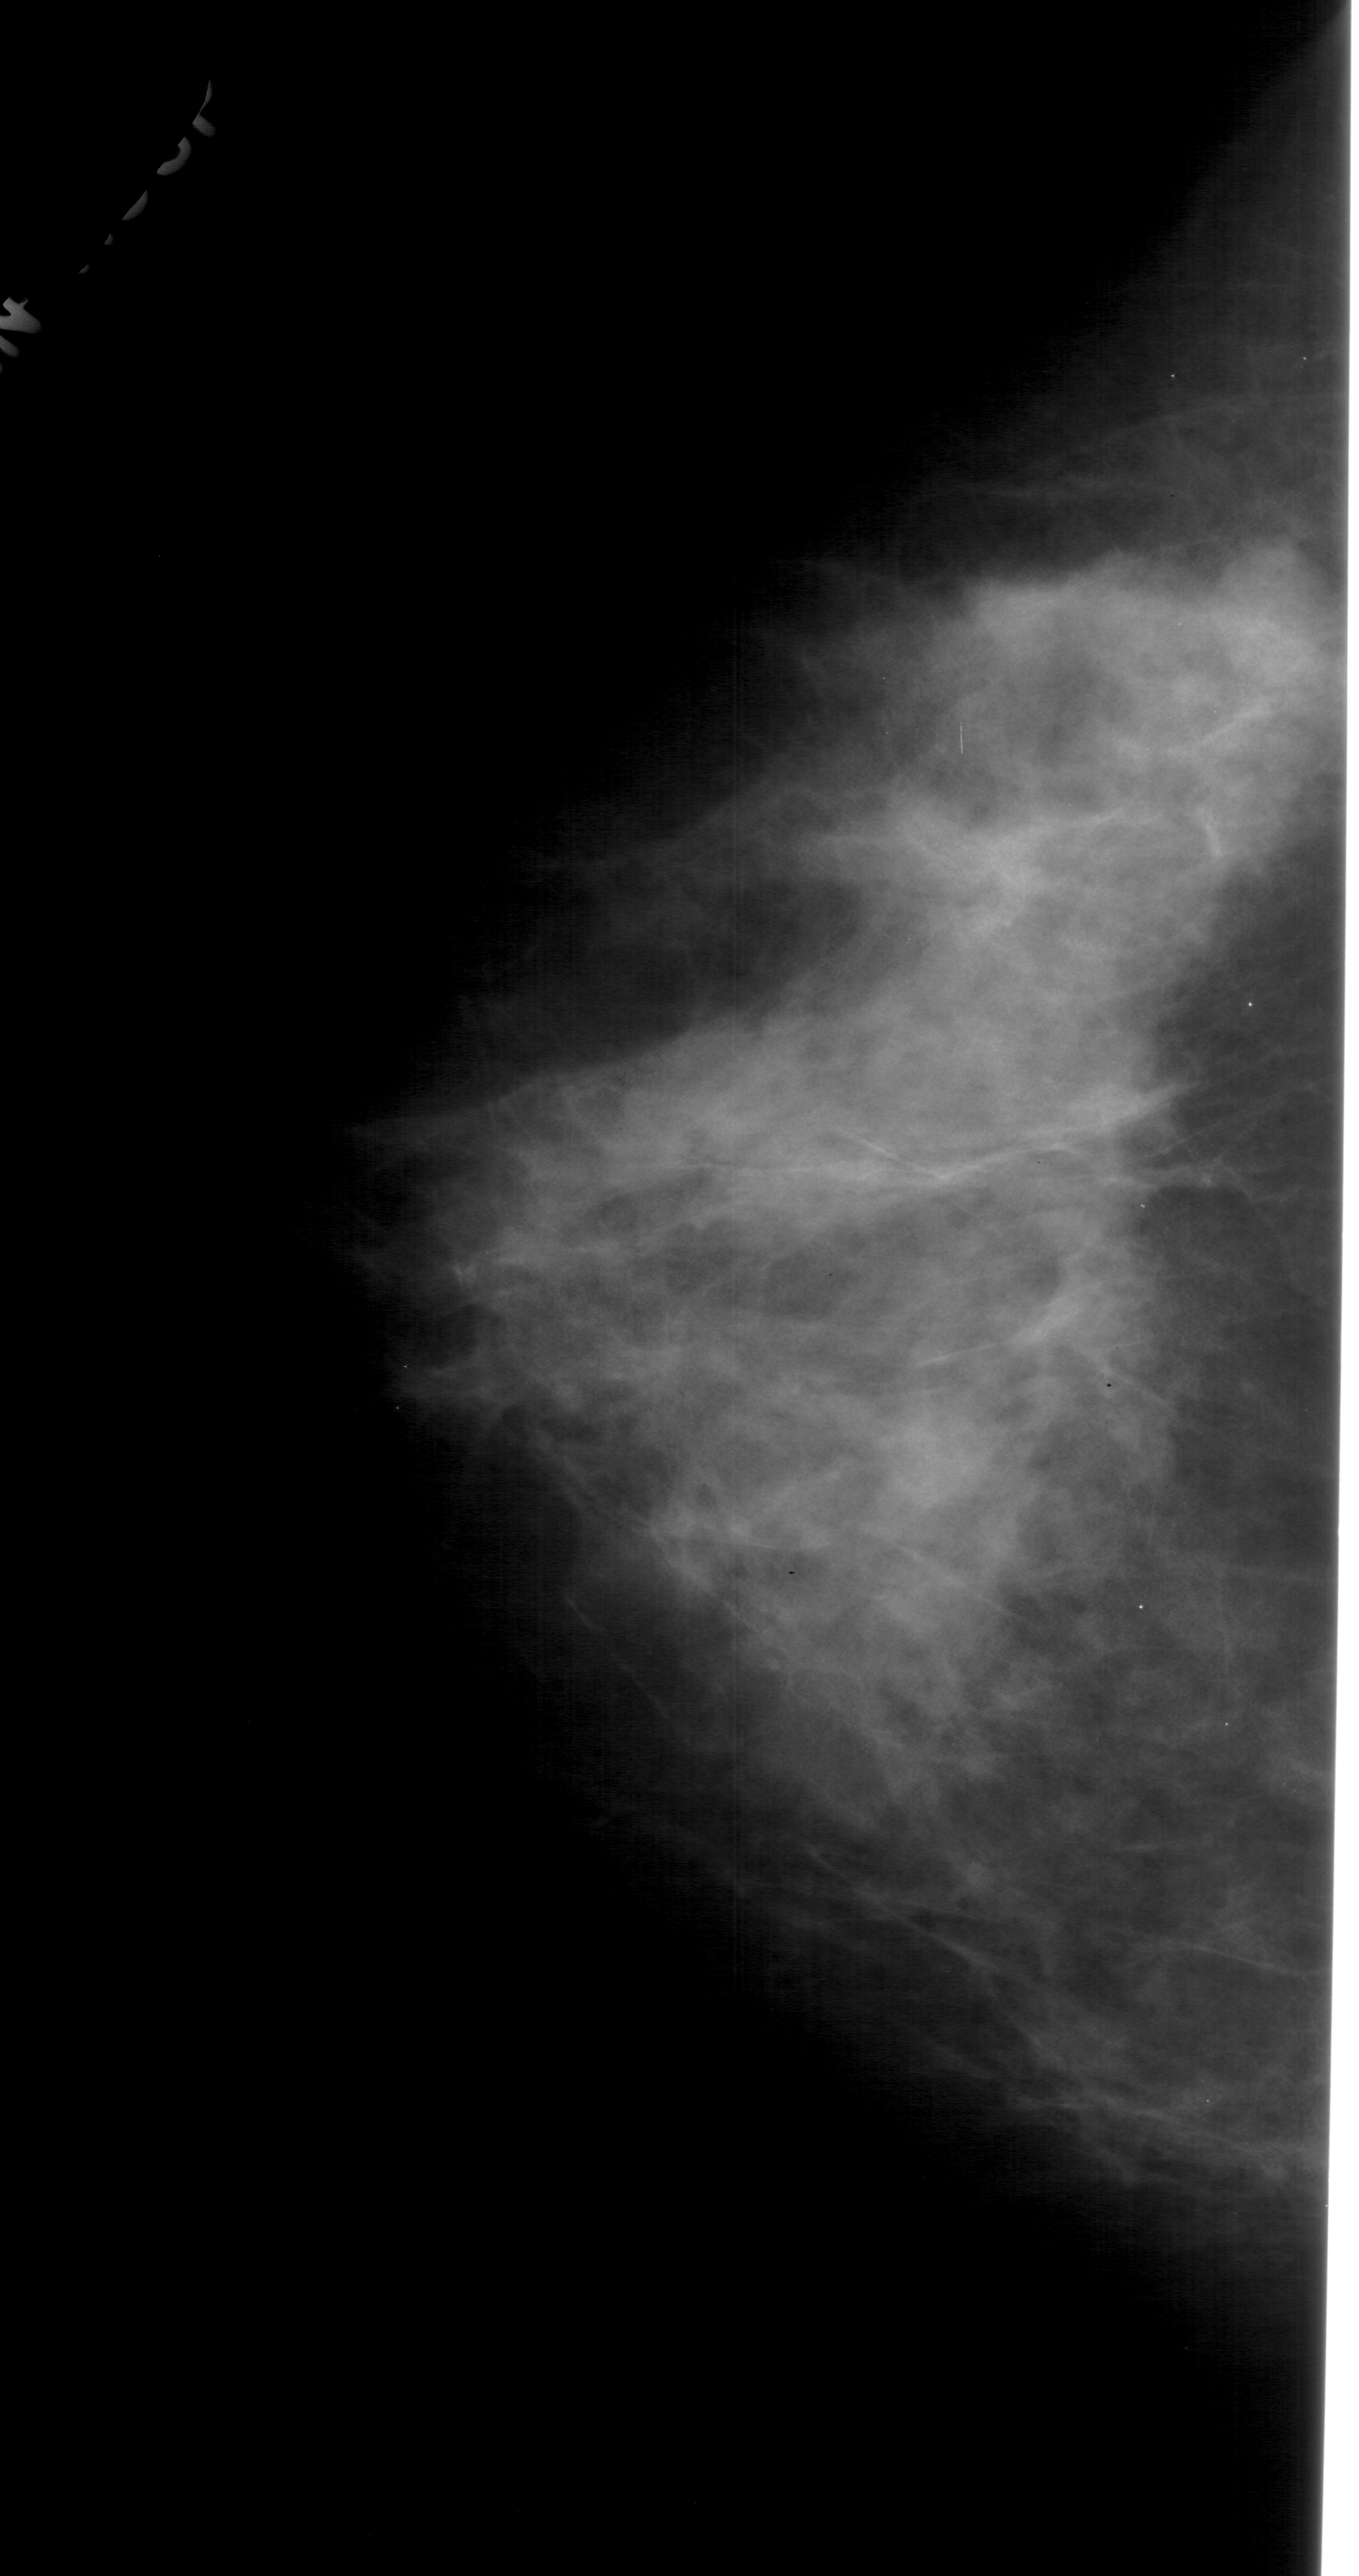
Scanned film-screen mammogram, left breast, CC view, breast composition: heterogeneously dense (BI-RADS density category 3 of 4).
Mass, shape round, margins obscured; BI-RADS assessment category 4; subtlety rating 4 on a 1 (subtle) to 5 (obvious) scale; pathology (as recorded): benign.